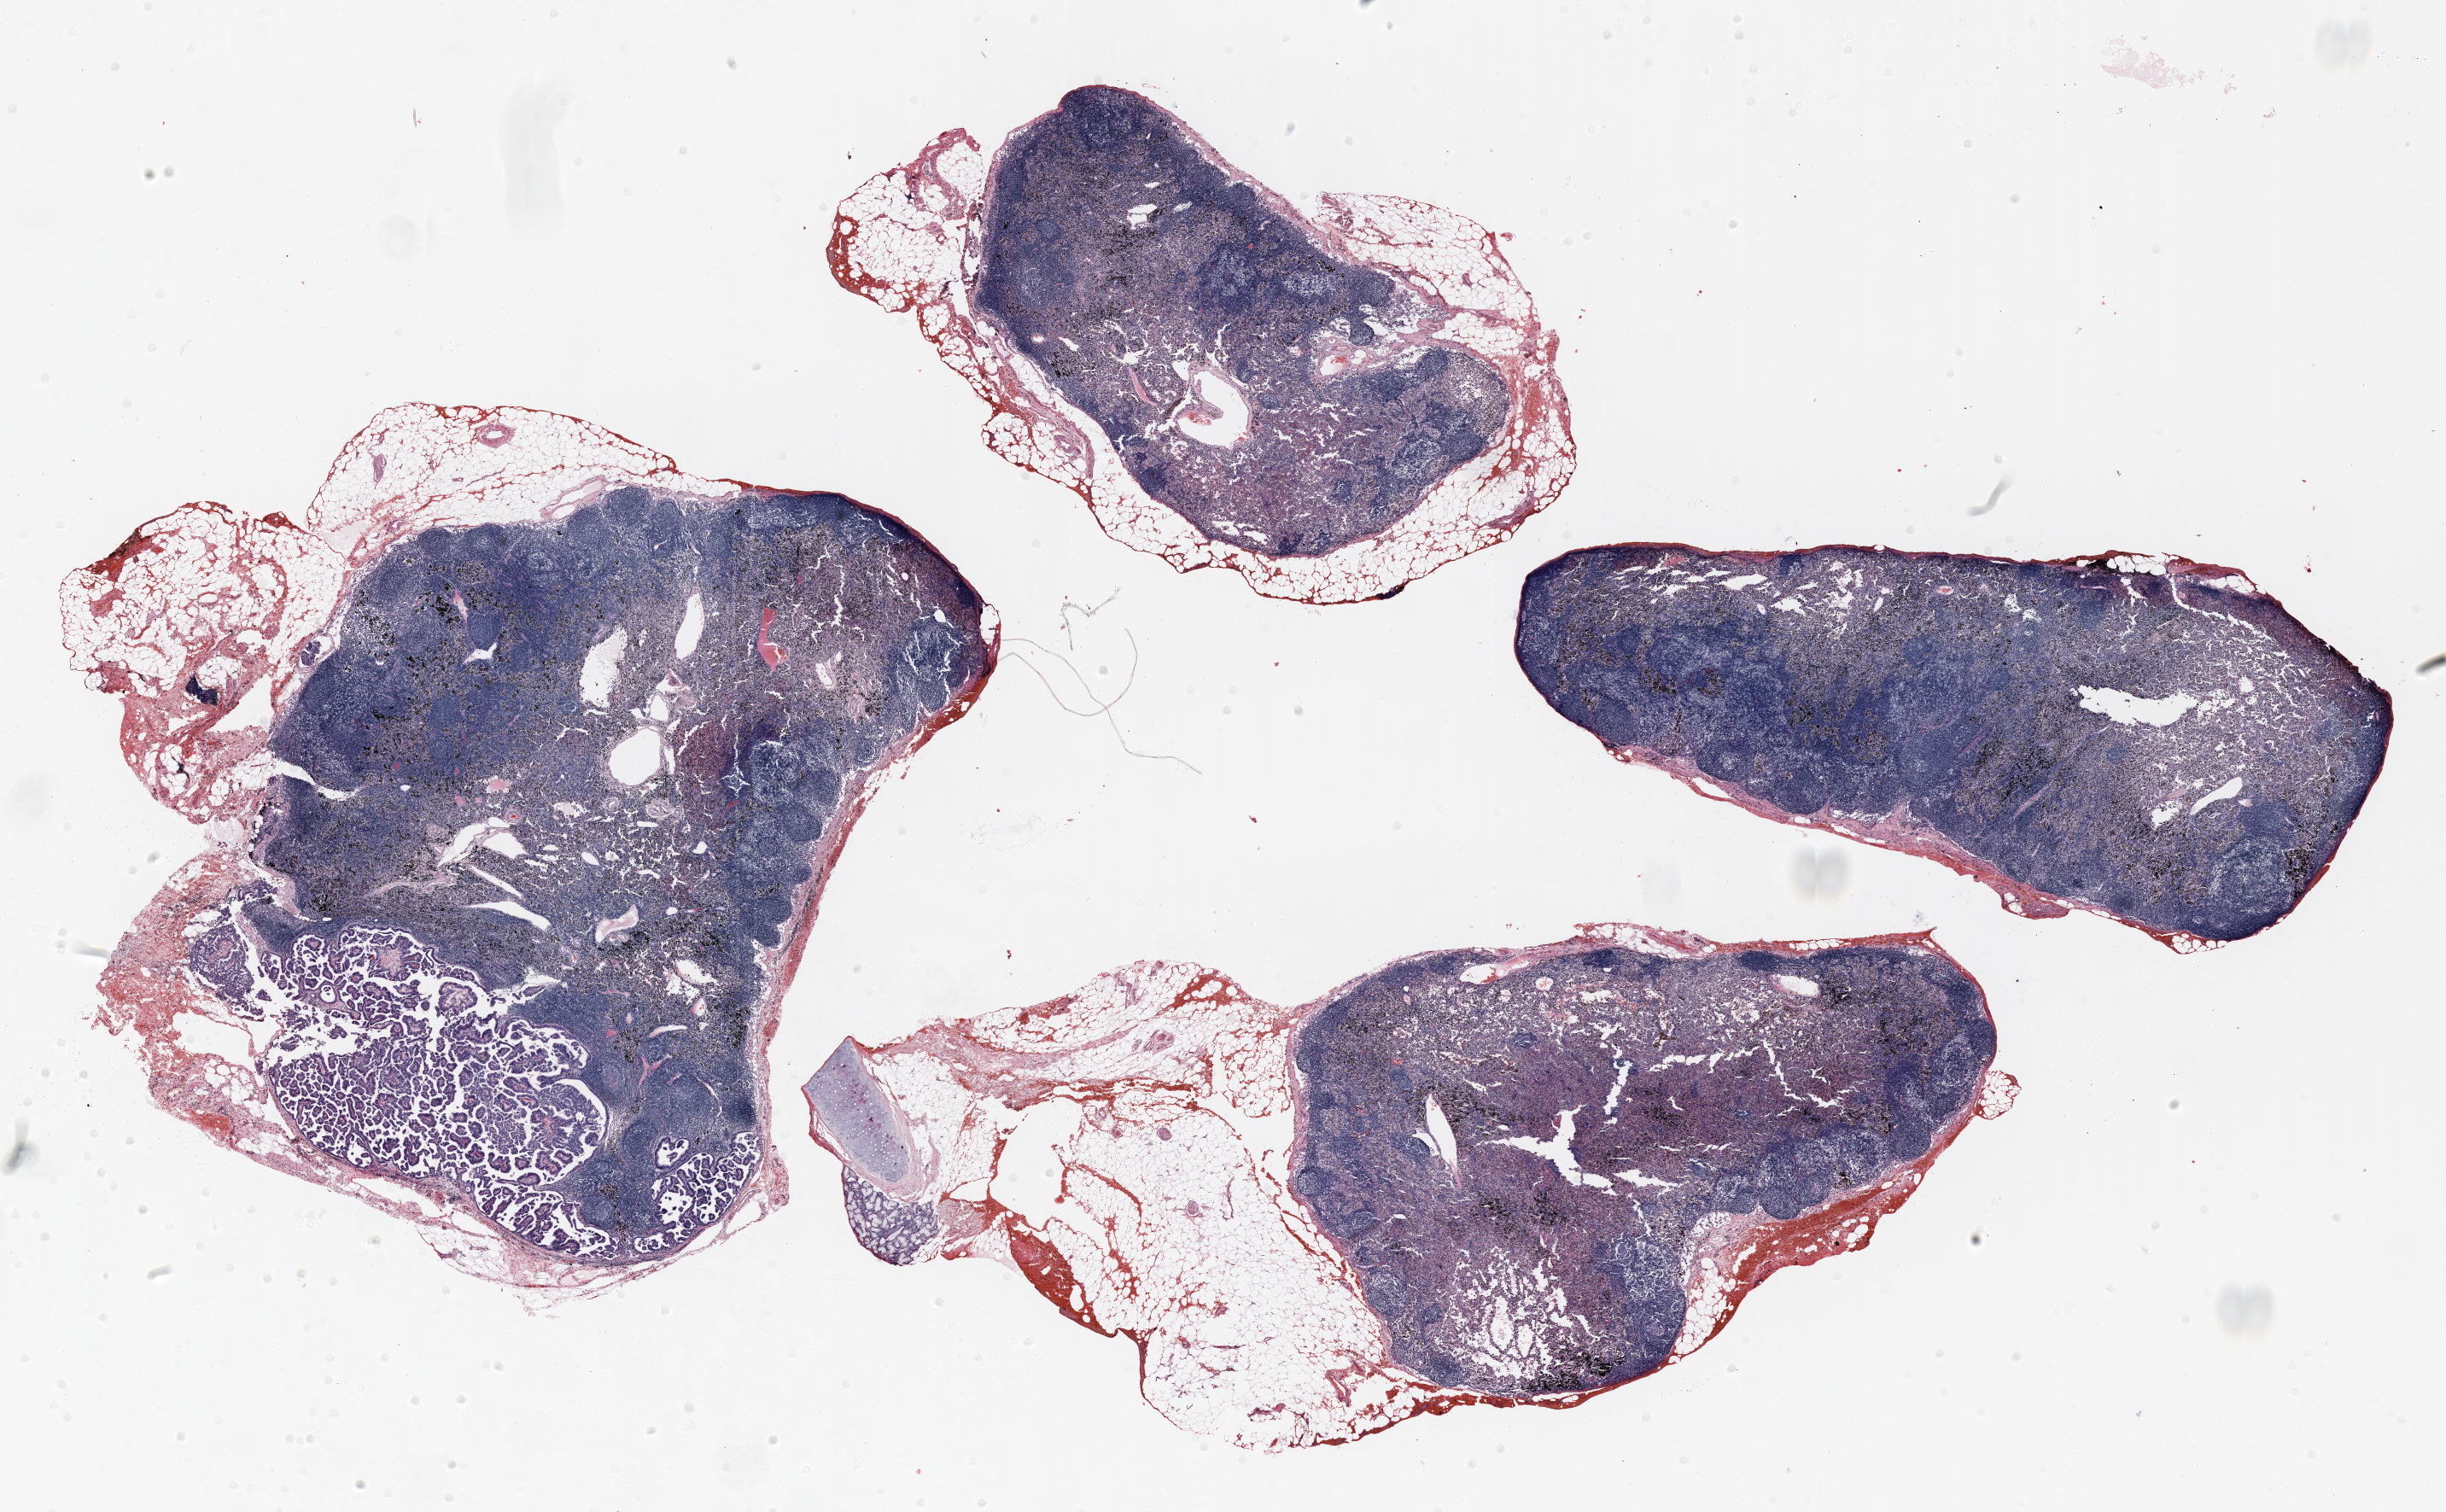
Whole-slide histology image, Hematoxylin and eosin (H&E) stained — a low-resolution overview of the entire scanned area, about 23.0 x 14.2 mm (acquisition: 20x scan). Formalin-fixed paraffin-embedded (FFPE) section. Lung. Female patient, aged 67 at enrolment. Former smoker at enrolment. Grade: moderately differentiated (G2).
• participant's lung-cancer diagnosis: Adenocarcinoma, NOS (ICD-O-3 8140/3)
• ICD-O-3 topography: upper lobe of lung (C34.1)
• stage (AJCC 6th edition): IIA
• primary tumour location (clinical record): left upper lobe
• tumour size (pathology): 23 mm